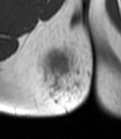
MRI of an extremity soft-tissue mass, one axial slice. Slice 14 of 47 in the series (ordered by position). MR volume resampled by the dataset authors to the PET/CT grid (not the native acquisition matrix). 3.27 mm slice thickness. 121 × 139 image matrix, field of view 118 × 136 mm. Female patient. Case-level facts recorded for this patient, not image findings: histological type: epithelioid sarcoma; grade: intermediate; site of the primary tumour: right buttock.
Structures marked on this image (expert contour drawn on MRI and transferred to this co-registered scan by the dataset authors):
- gross tumour volume including surrounding oedema: bounding box [x1, y1, x2, y2] px = [36, 45, 92, 112]
- gross tumour volume (mass): [47, 54, 69, 74]